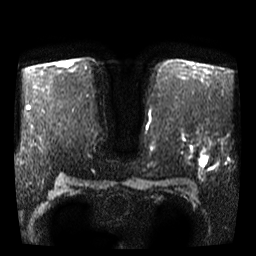
Breast MRI, one axial slice; slice 28 of 46 in the series (ordered by position); diffusion-weighted series; image 2 of 4 stored at this slice position (different b-values; order by instance number); 3 T; 256 × 256 image matrix, field of view 340 × 340 mm. Female patient.
Annotated regions visible in this slice (manually delineated by an expert):
- tumour on diffusion-weighted imaging: box from (x=199, y=157) to (x=206, y=167) px